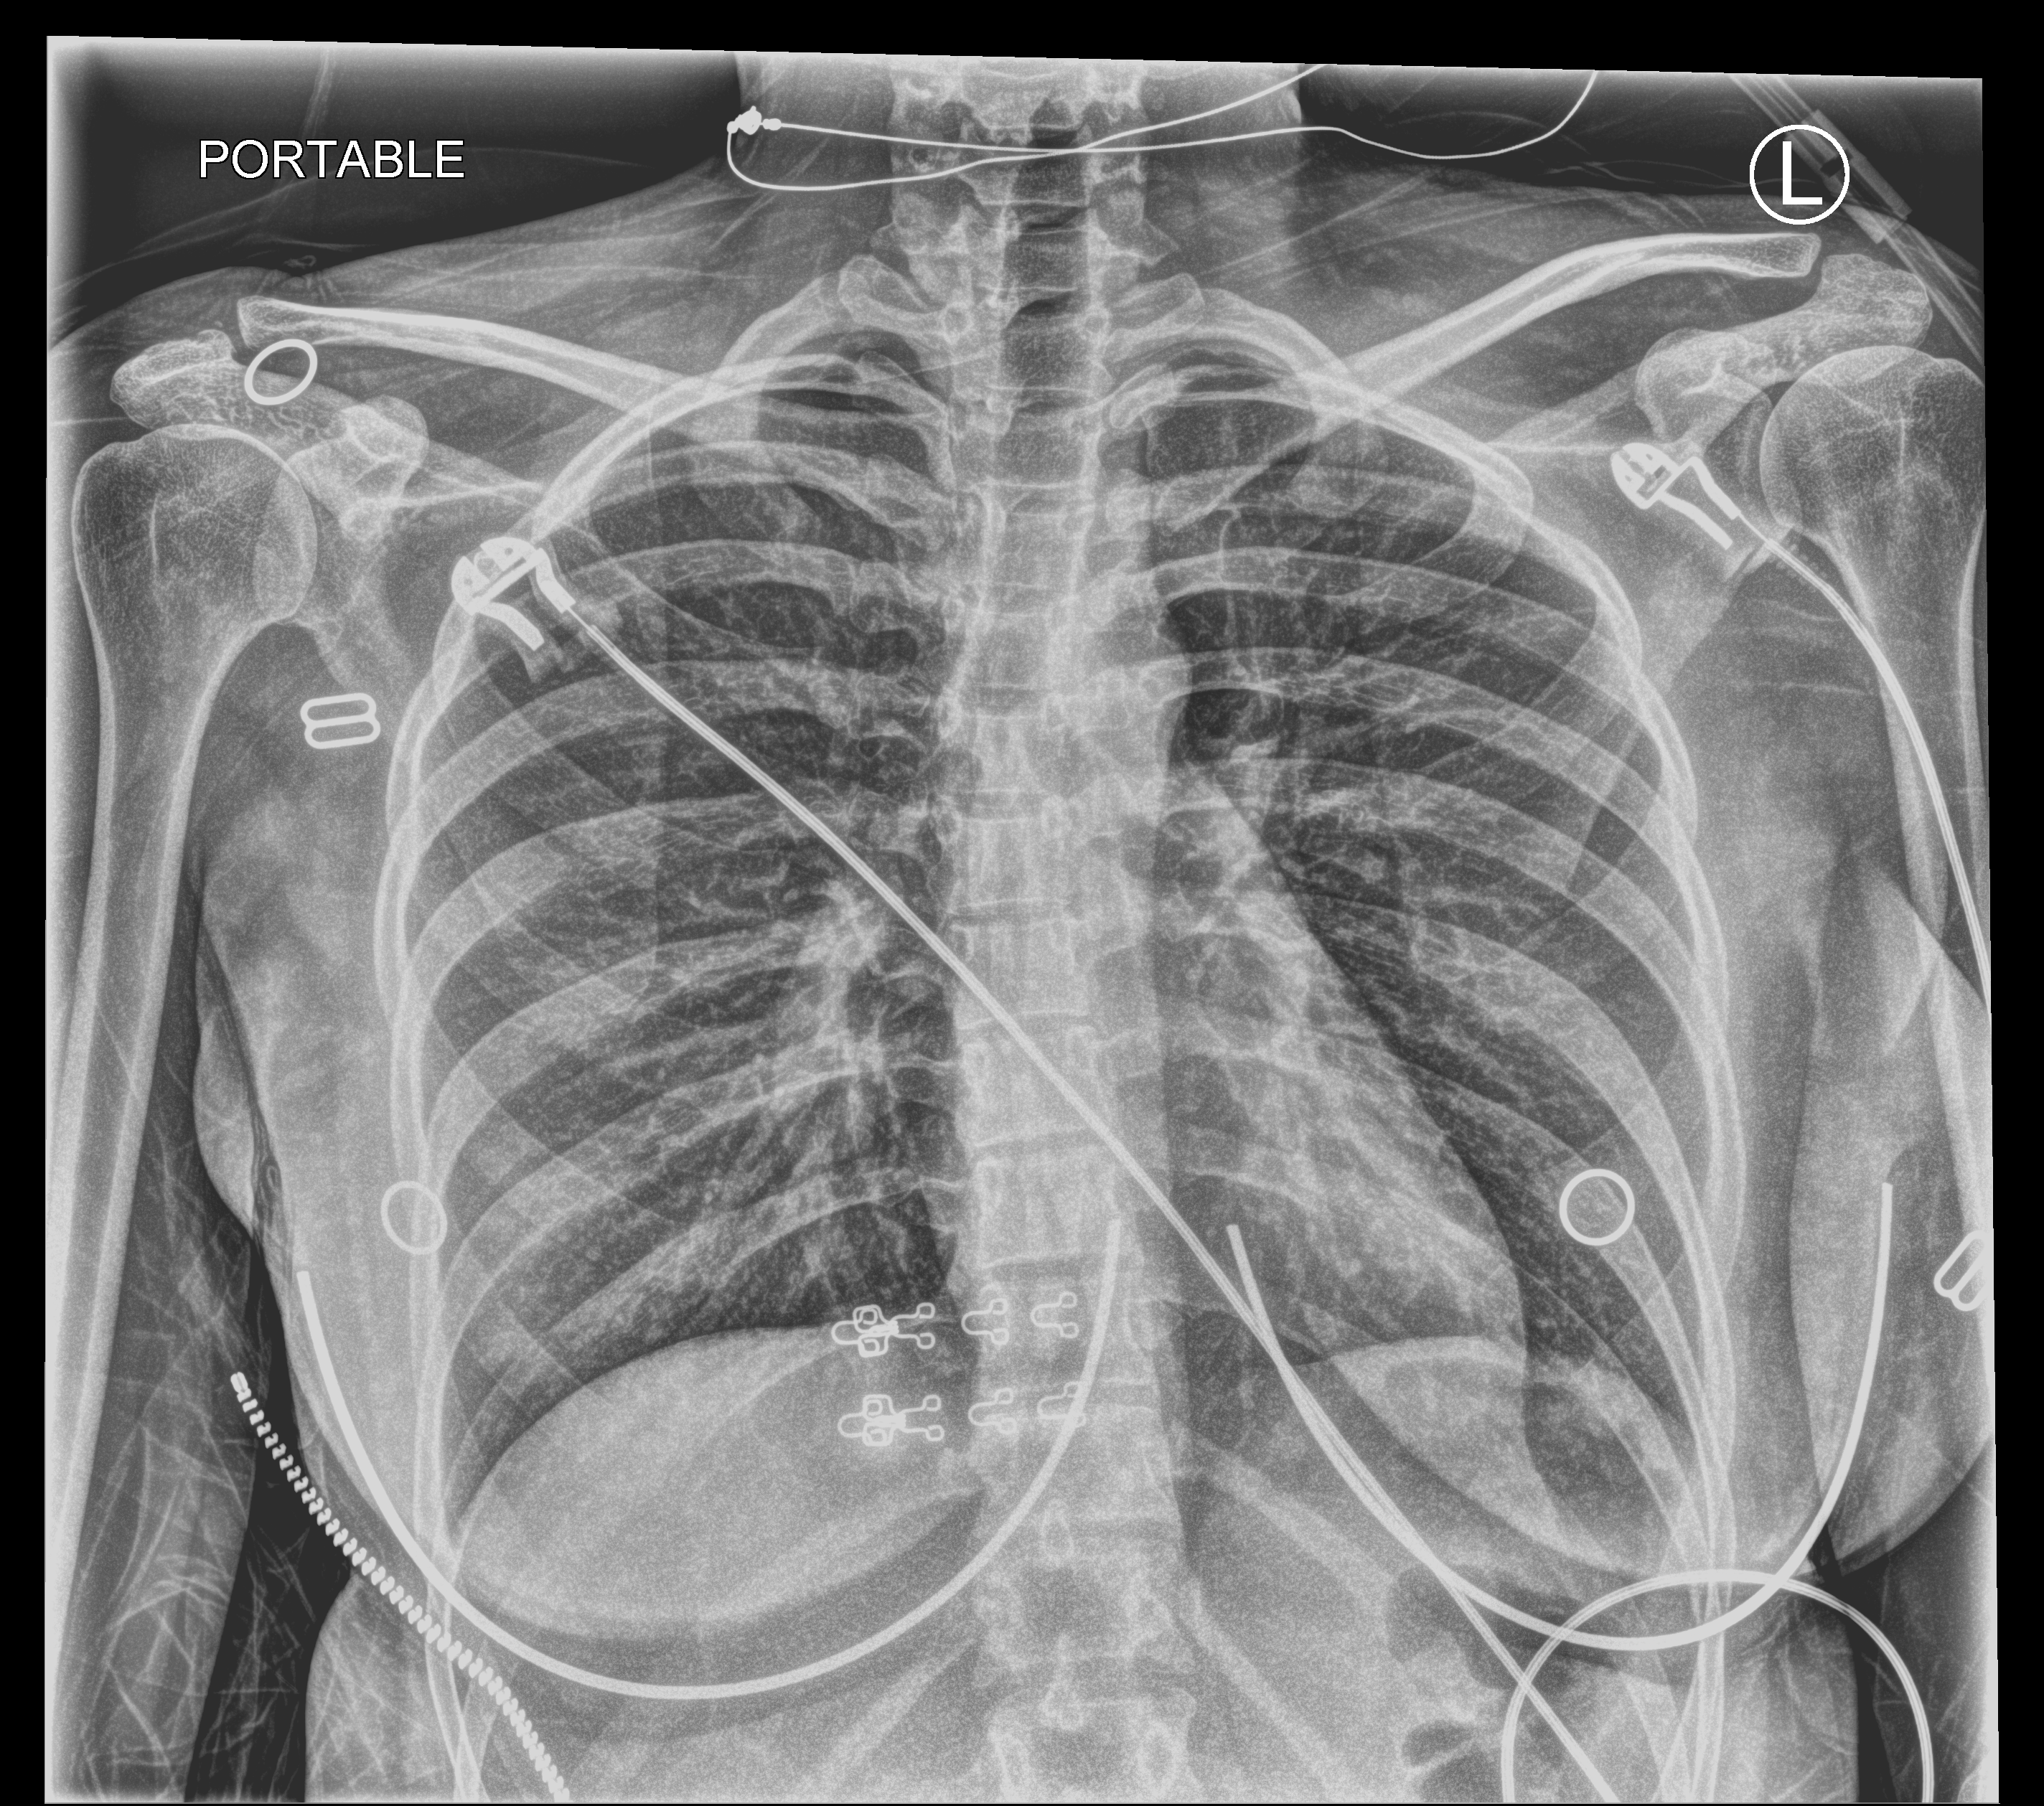
Portable chest radiograph. Patient hospitalised with COVID-19; female, aged 18–59 years.
Admission-level facts for this patient (not findings on this image; timing relative to this image not recorded): length of hospital stay: 1 day; admitted to intensive care during this hospital stay: no; mechanically ventilated during this hospital stay: no.